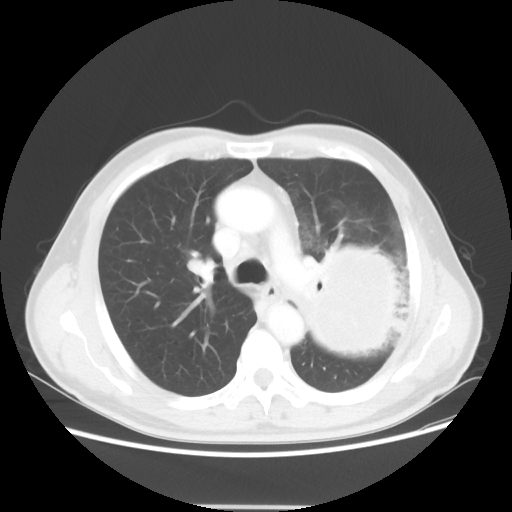
Chest CT, one axial slice; position 35 of 53 along the scan axis; reconstruction kernel STANDARD; lung window (W 1500 / L -600 HU); 512 × 512 image matrix, field of view 391 × 391 mm. Patient: male, 60 years. From the clinical record (not read from this slice): clinical TNM (as recorded): T4 N1 M1a.
Annotated regions visible in this slice (rectangle marked by the reading radiologist):
- lung tumour (recorded histology: large cell carcinoma): bounding box <289,234,409,368> (left, top, right, bottom; pixels)